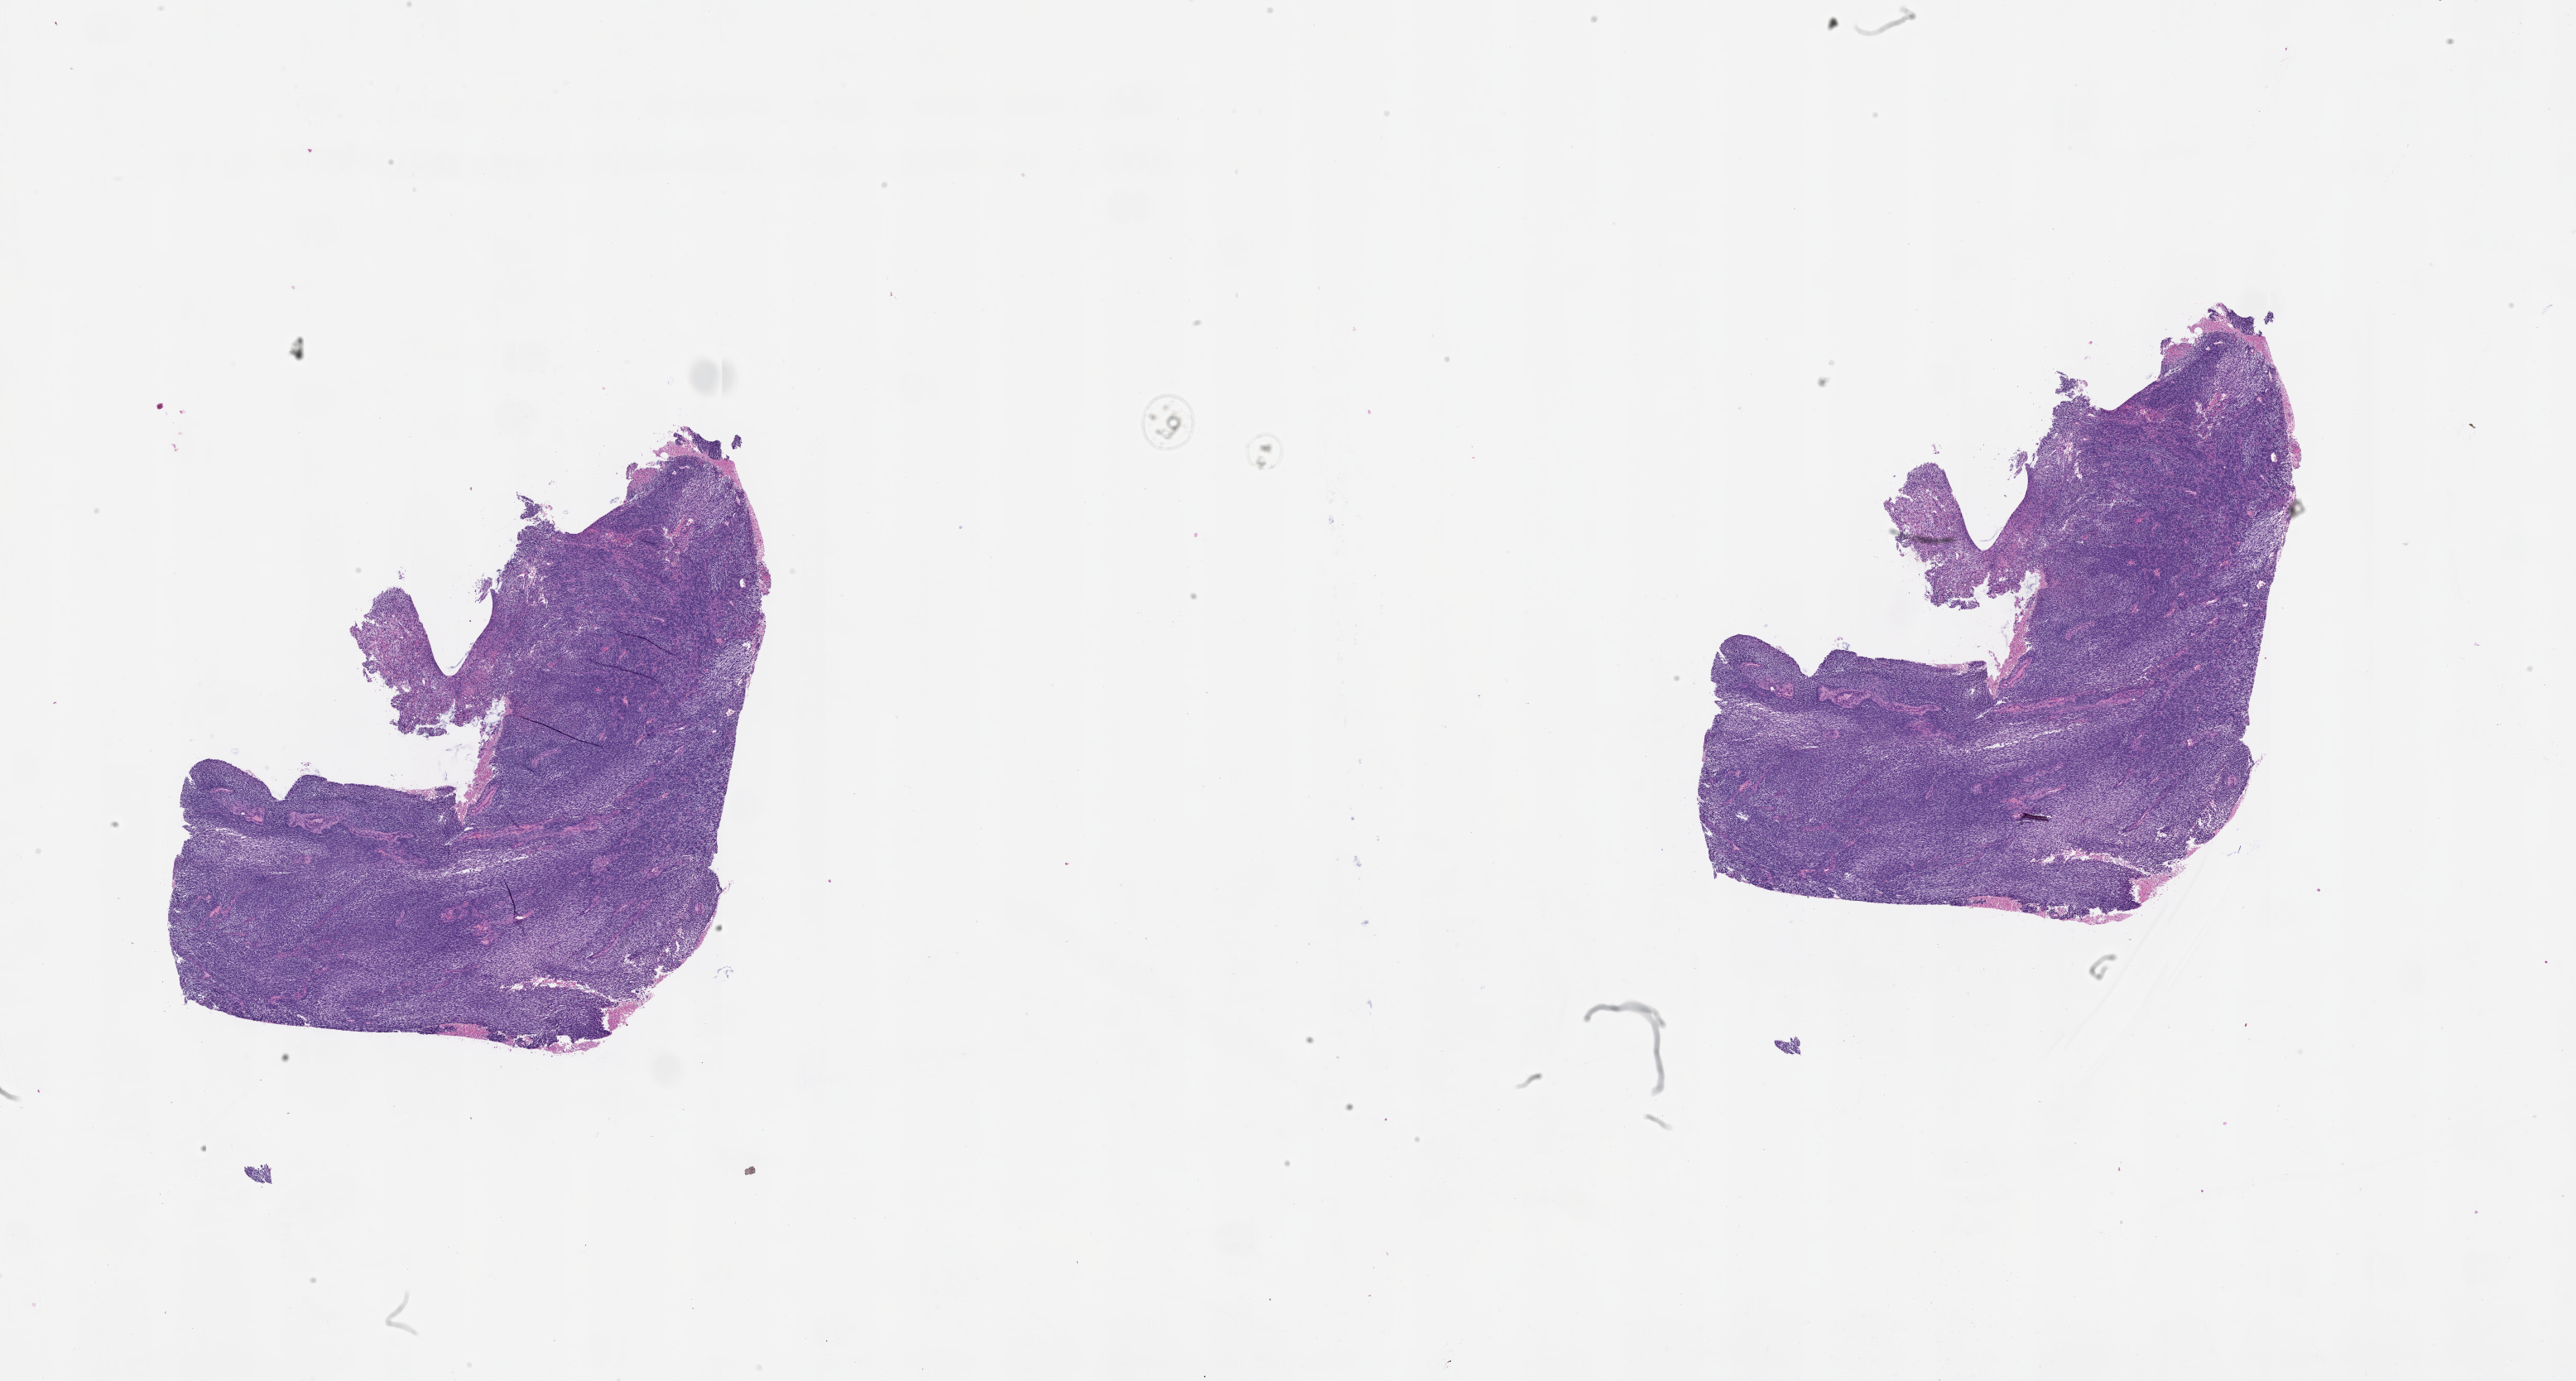
Digitized H&E-stained tissue section (whole slide), a low-resolution overview of the entire scanned area, about 25.1 x 13.4 mm (acquisition: 20x scan).
Patient diagnosis (cohort enrolment): sarcoma (site not recorded at cohort level).